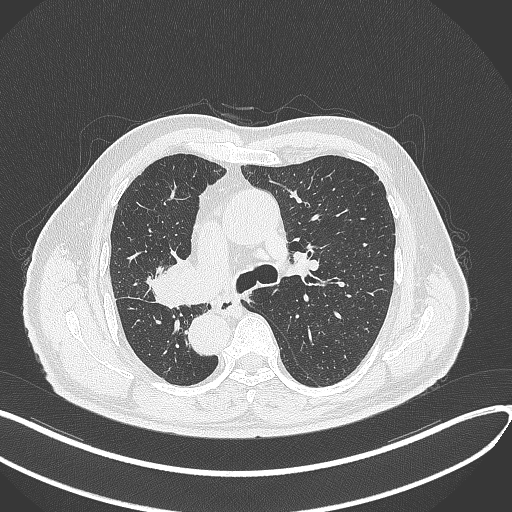
Chest CT, one axial slice; position 192 of 300 along the scan axis; lung window (W 1500 / L -600 HU); 512 × 512 image matrix, field of view 400 × 400 mm. Patient: male, 67 years. Case-level facts recorded for this patient, not image findings: clinical TNM (as recorded): T2a N0 M0.
Annotated regions visible in this slice (rectangle marked by the reading radiologist):
- lung tumour (recorded histology: squamous cell carcinoma): box from (x=145, y=251) to (x=209, y=311) px